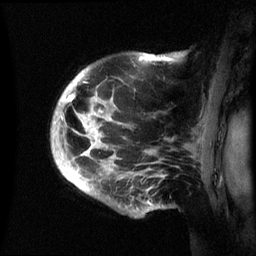
Breast MRI (dynamic contrast-enhanced), one sagittal slice. Slice 48 of 60 in the series (ordered by position). Dynamic contrast-enhanced series, image 2 of 3 at this slice position (ordered by acquisition). 1.5 T. TE 4.2 ms, TR 8.4 ms. 2.4 mm slice thickness. 256 × 256 image matrix, field of view 230 × 230 mm. Female patient, age 48 years.
Outlined on this slice (semi-automatically segmented with operator editing):
- analysis volume of interest (the breast-tissue region the enhancement analysis was run in; not a lesion): bounding box (x1, y1, x2, y2) in pixels: (51, 53, 187, 217)
- tumour enhancement mask (voxels above the 70 % enhancement threshold inside the analysis volume of interest): (61, 55, 156, 204)